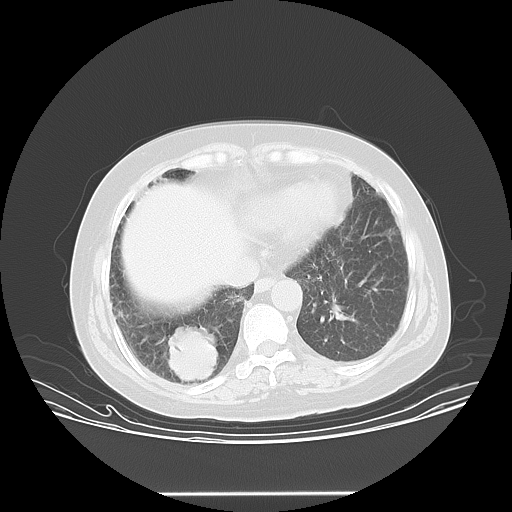
Chest CT, one axial slice; position 9 of 45 along the scan axis; reconstruction kernel LUNG; lung window (W 1500 / L -600 HU); 5 mm slice thickness; 512 × 512 image matrix. Female patient, age 55 years. Case-level facts recorded for this patient, not image findings: clinical TNM (as recorded): T2 N0 M1b.
Annotated regions visible in this slice (rectangle marked by the reading radiologist):
- lung tumour (recorded histology: squamous cell carcinoma): box from (x=164, y=326) to (x=221, y=394) px